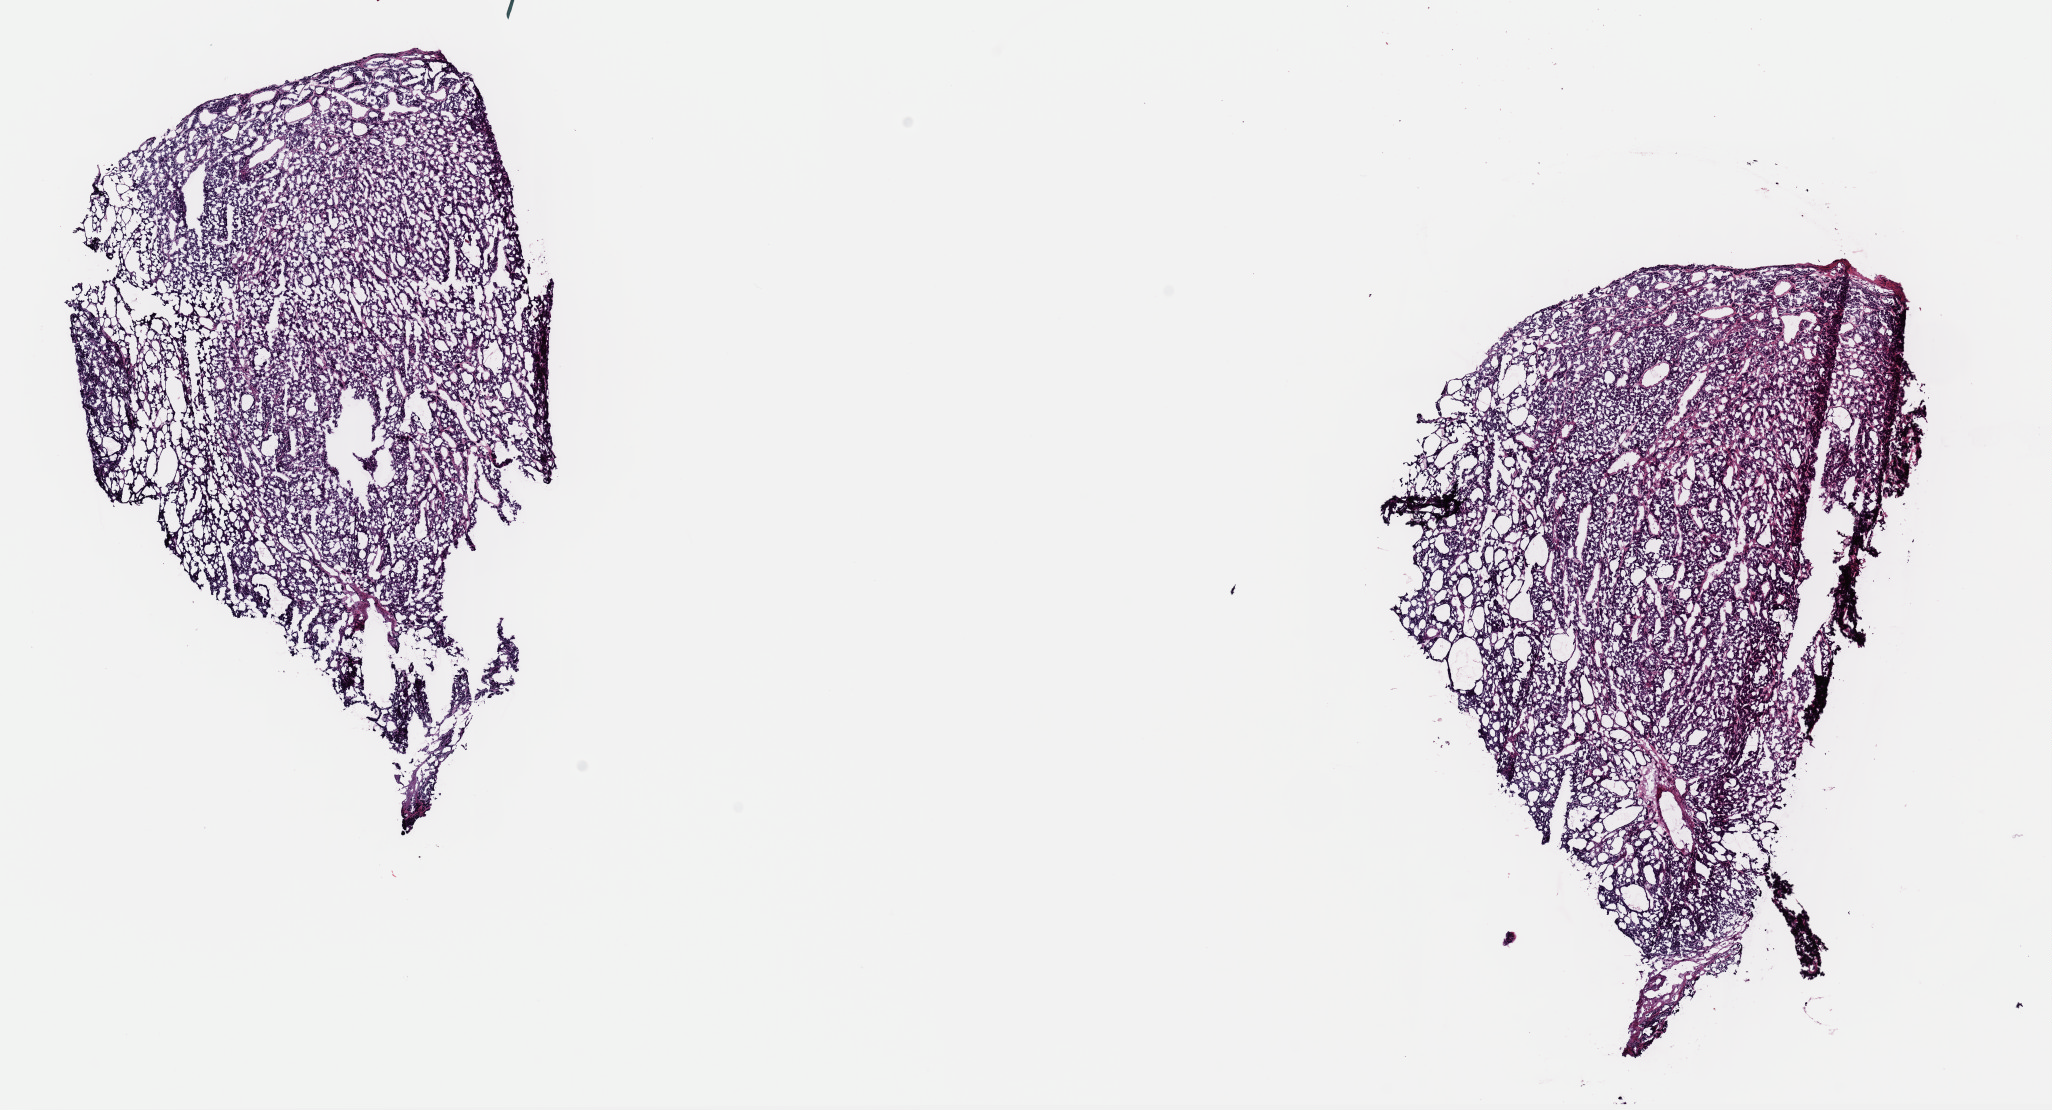
Whole-slide histology image, H&E — a low-resolution overview of the entire scanned area, about 16.2 x 8.8 mm. Frozen section from the top of the tissue portion. Primary tumour sample from the thyroid. Male, age 62 years at initial diagnosis. Composition of this section per pathologist review: tumour cells 90%, tumour nuclei 90%, normal cells 0%, stromal cells 10%, necrosis 0%. Infiltration values recorded for this section: lymphocyte infiltration 0%, monocyte infiltration 0%, neutrophil infiltration 0%.
- AJCC pathologic stage: IVC (7th edition)
- lymph nodes positive (case pathology): 0 of 3 examined
- pathologic diagnosis: Papillary carcinoma, follicular variant (thyroid gland)